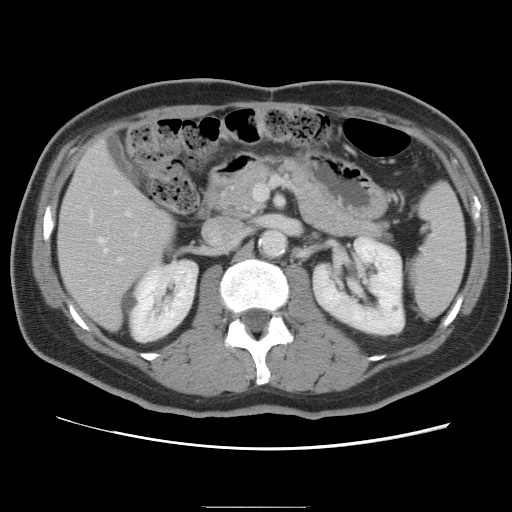
Contrast-enhanced abdominal CT, one axial slice; slice 38 of 87 in the series (ordered by position); 120 kVp; intravenous contrast given; soft-tissue window (W 400 / L 40 HU); 5 mm slice thickness; 512 × 512 image matrix, field of view 363 × 363 mm. Male patient, age 63 years. Case-level facts recorded for this patient, not image findings: diagnosis: colorectal cancer liver metastases, imaged before liver resection; multiple liver metastases: no; largest metastasis: 9 cm; disease in both lobes: no.
Structures marked on this image (manually delineated by an expert):
- hepatic veins: box from (x=99, y=191) to (x=116, y=251) px
- liver: (x=59, y=142)–(x=174, y=329)
- planned liver remnant (the part of the liver to remain after resection): (x=59, y=142)–(x=174, y=329)
- portal vein (with intrahepatic branches): (x=104, y=210)–(x=132, y=293)